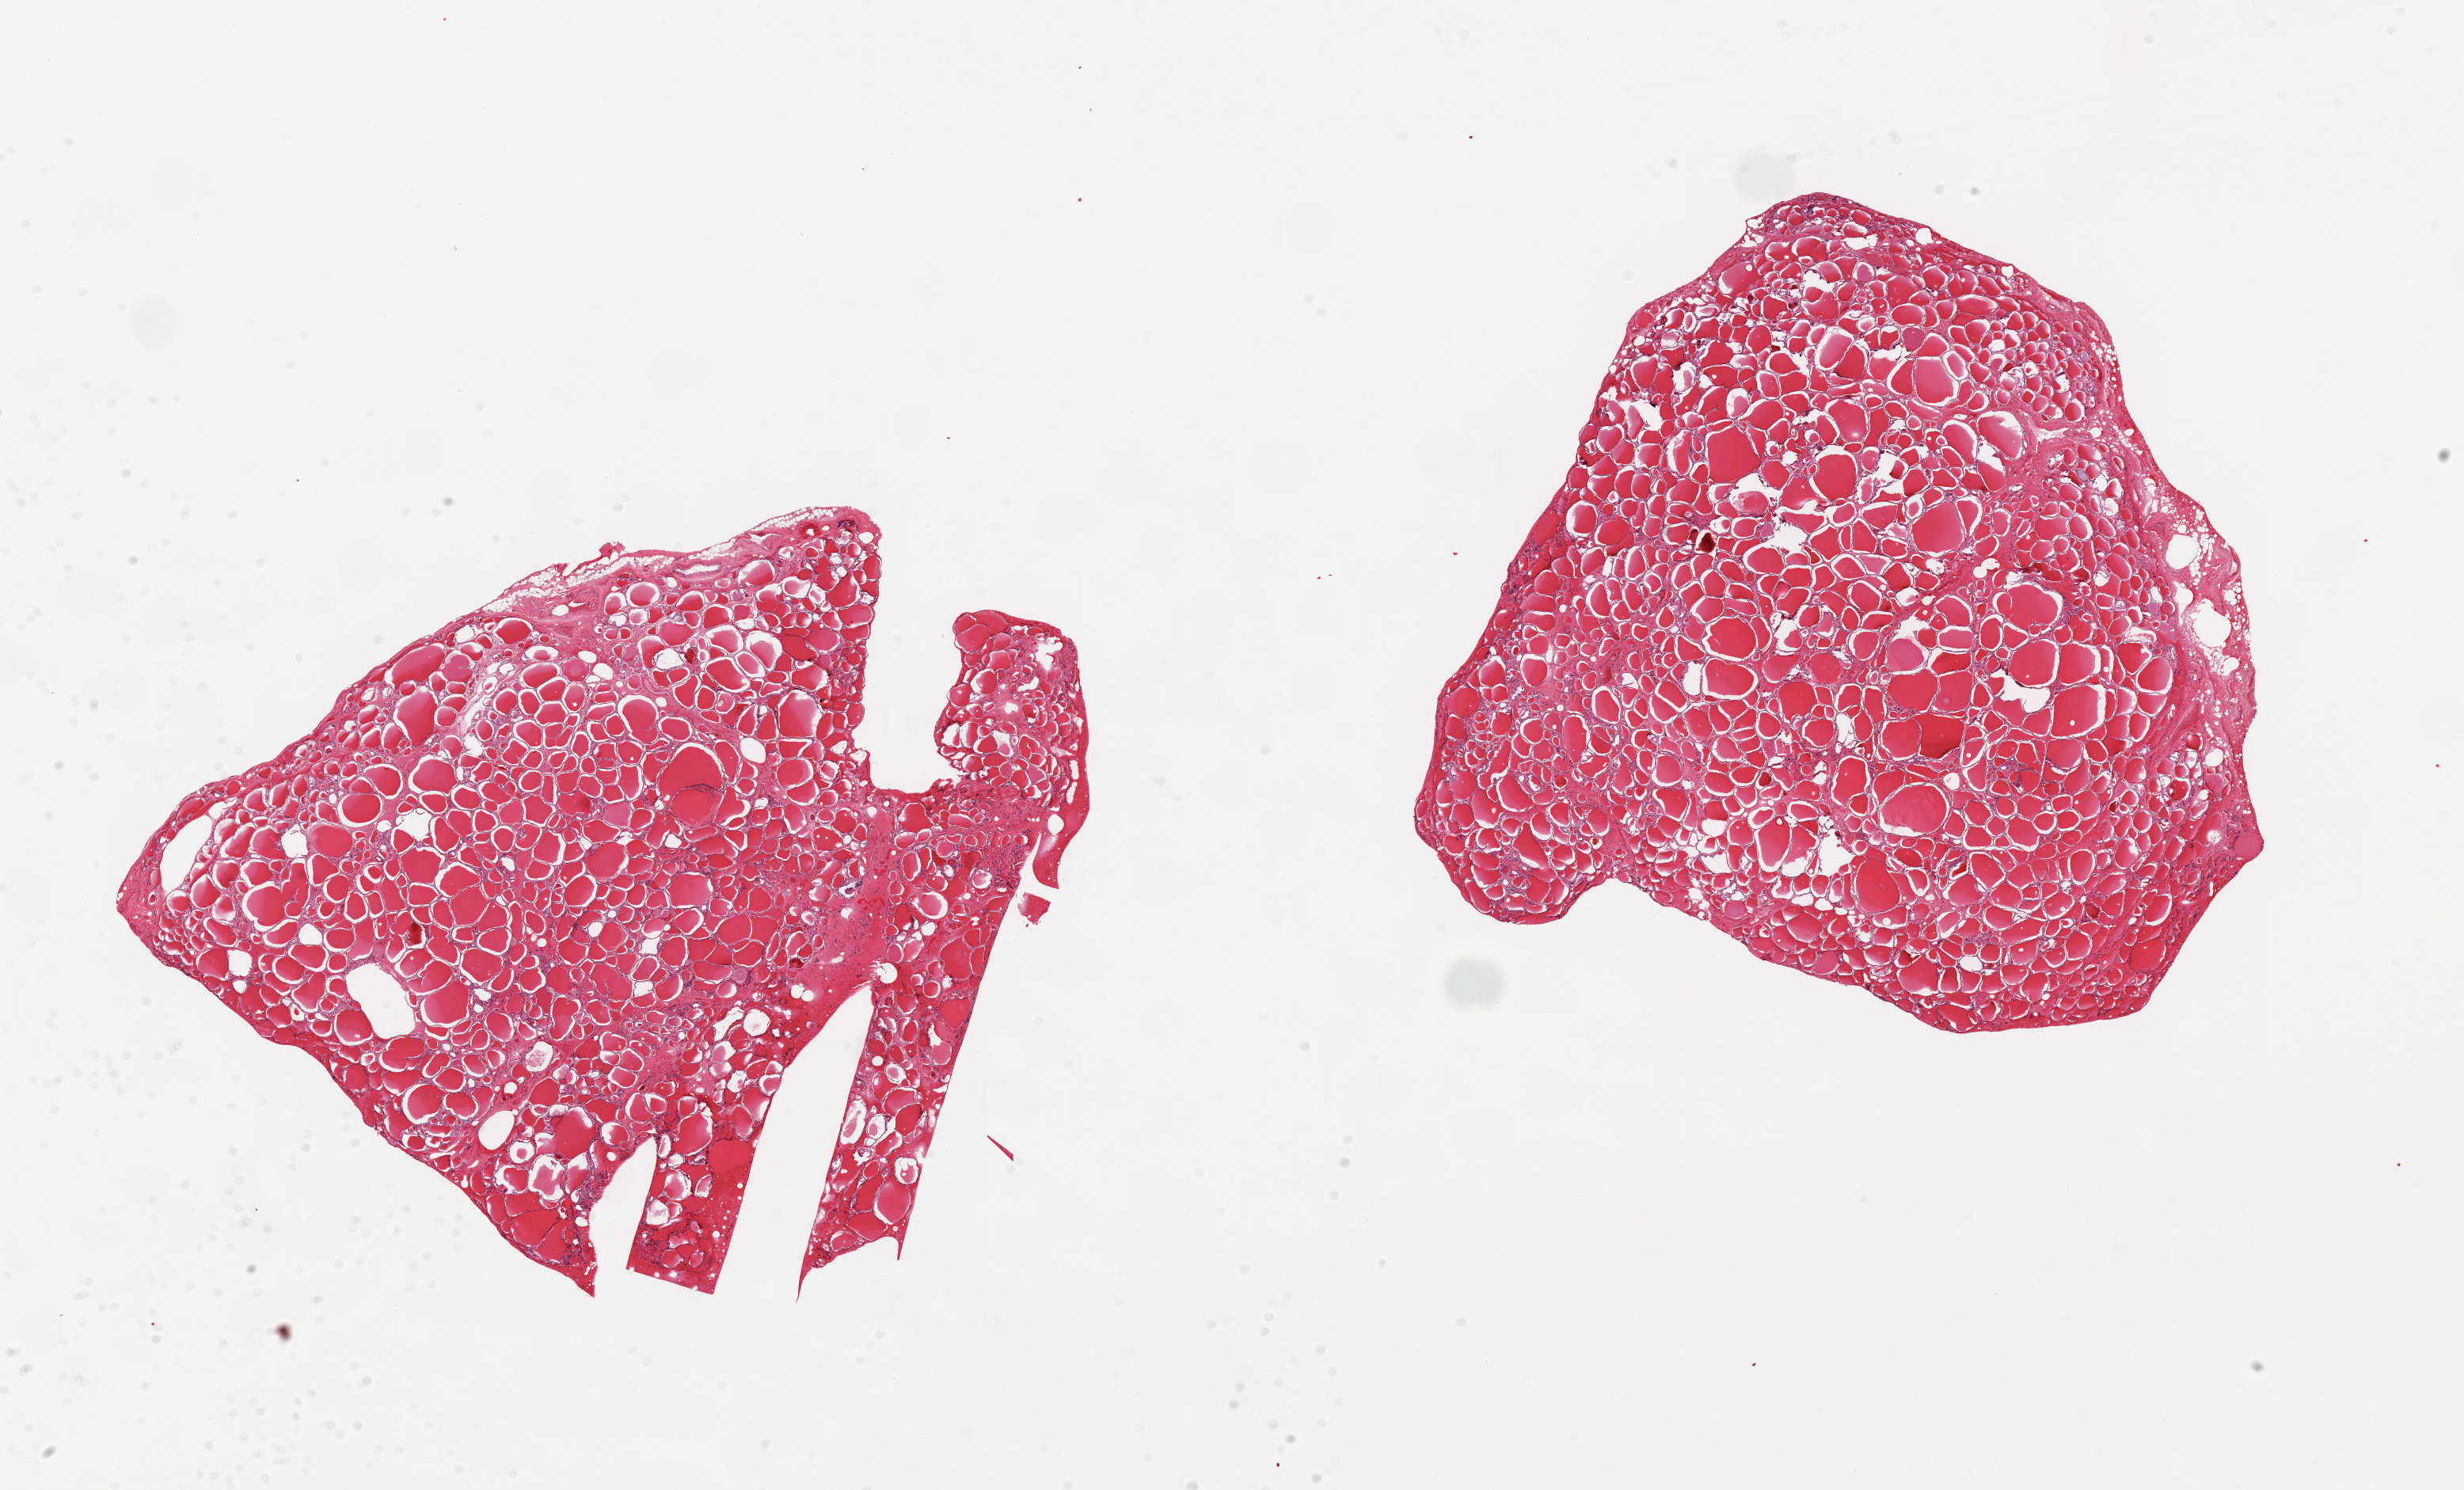
Whole-slide image, H&E stain, brightfield — a low-resolution overview of the entire scanned area, about 24.6 x 14.9 mm (slide scanned at 20x), PAXgene-fixed, paraffin-embedded tissue, target tissue: thyroid, tissue donor sample. Donor: female.
Pathologist's review note for this sample: 2 pieces, no abnormalities.